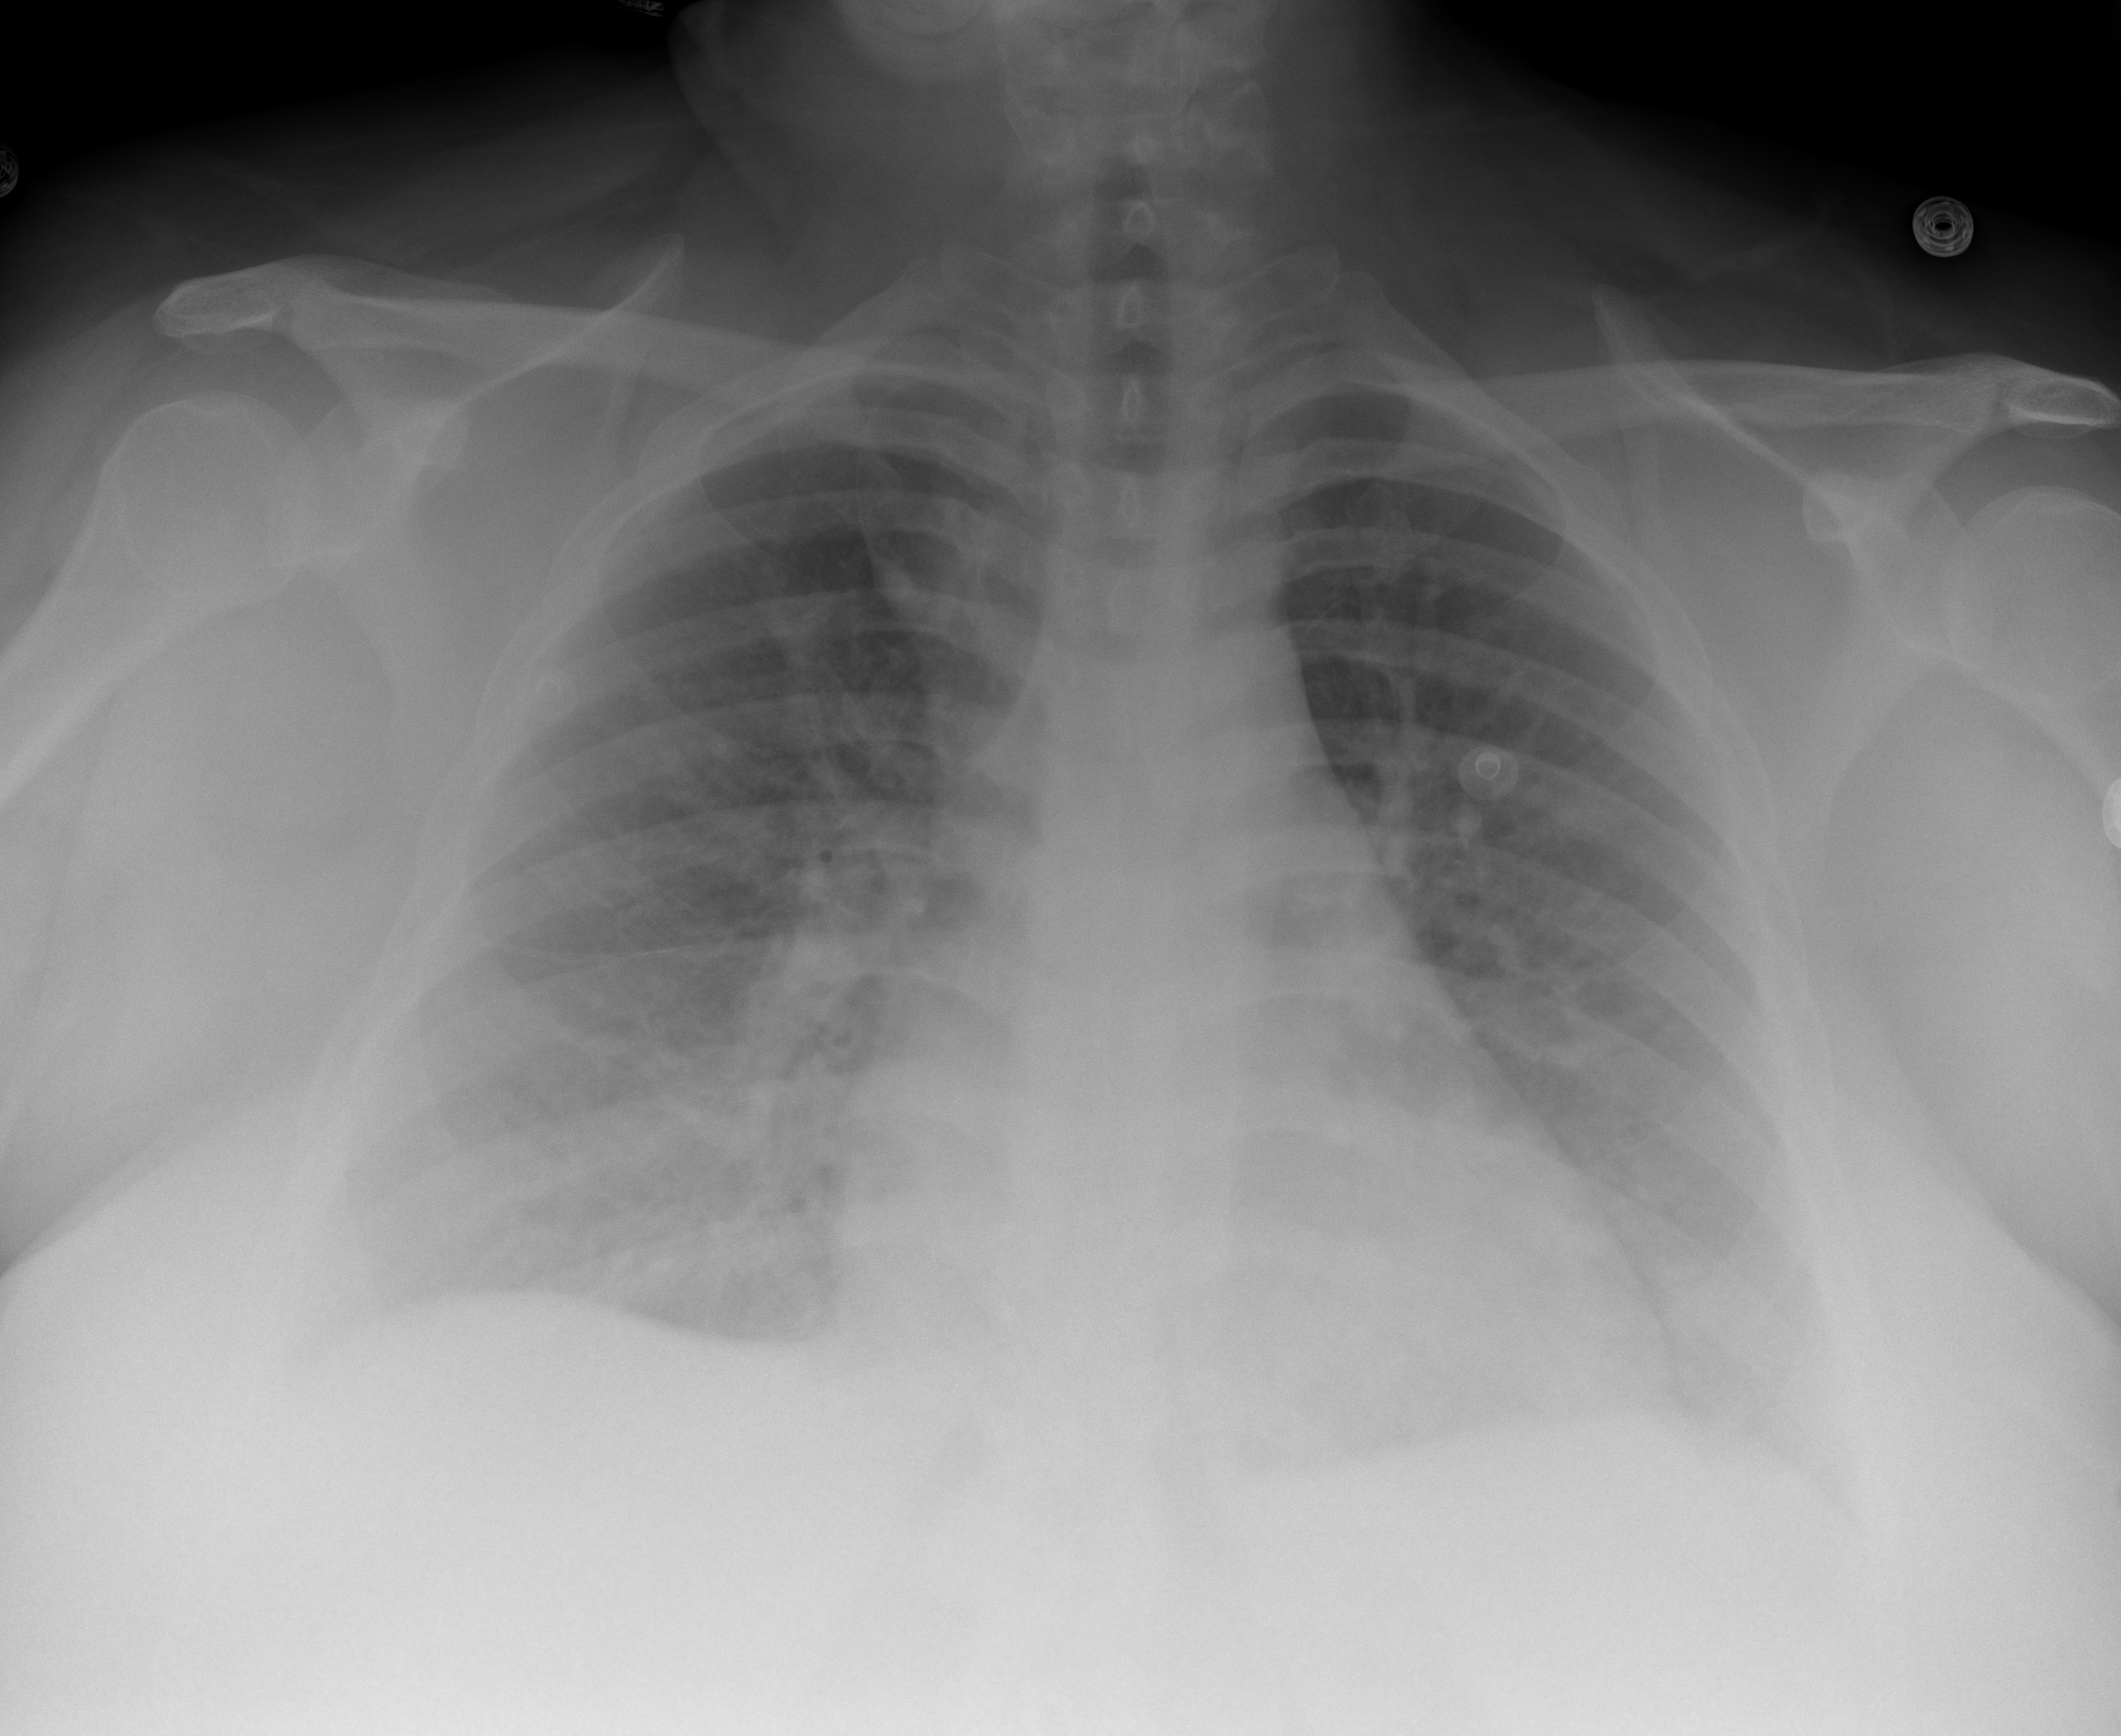
Portable chest radiograph, AP projection. Female patient, age 37 years; COVID-19 (test-positive).
Key findings recorded by the radiologist: No acute disease.